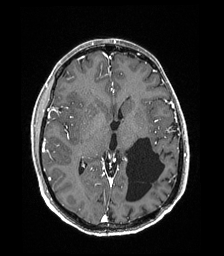
Brain MRI from a brain-tumour surgery series, one axial slice; position 97 of 192 along the scan axis; T1-weighted post-contrast; 1 mm slice thickness; 224 × 256 image matrix, field of view 224 × 256 mm. From the clinical record (not read from this slice): histopathology: Low grade glioma; IDH mutation: no; tumour location: Left Parieto-Occipital Intraventricular.
Structures marked on this image (expert manual segmentation):
- previous resection cavity: bounding box [x1, y1, x2, y2] px = [126, 137, 164, 202]